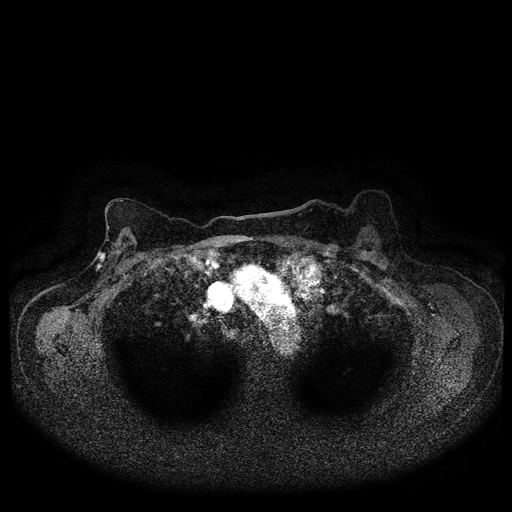
Breast MRI (dynamic contrast-enhanced, multi-phase), one axial slice. Position 71 of 116 along the scan axis. Dynamic contrast-enhanced series, time point 2 of 5 at this slice position (early post-contrast). 1.5 T. TE 2.7 ms, TR 5.4 ms. 2 mm slice thickness. 512 × 512 image matrix. Patient: female, 72 years.
Annotated regions visible in this slice (semi-automatic segmentation, software-assisted and operator-edited):
- breast lesion (labelled 'tumour' in the annotation; benign lesions carry a separate 'benign' label): bounding box <95,250,108,273> (left, top, right, bottom; pixels)